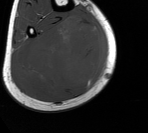
MRI of an extremity soft-tissue mass, one axial slice. Slice 66 of 76 in the series (ordered by position). MR volume resampled by the dataset authors to the PET/CT grid (not the native acquisition matrix). 3.27 mm slice thickness. 148 × 133 image matrix. Male patient. From the clinical record (not read from this slice): histological type: liposarcoma - round cell; grade: high; site of the primary tumour: right calf.
Annotated regions visible in this slice (expert contour drawn on MRI and transferred to this co-registered scan by the dataset authors):
- gross tumour volume (mass): bounding box <17,19,103,93> (left, top, right, bottom; pixels)